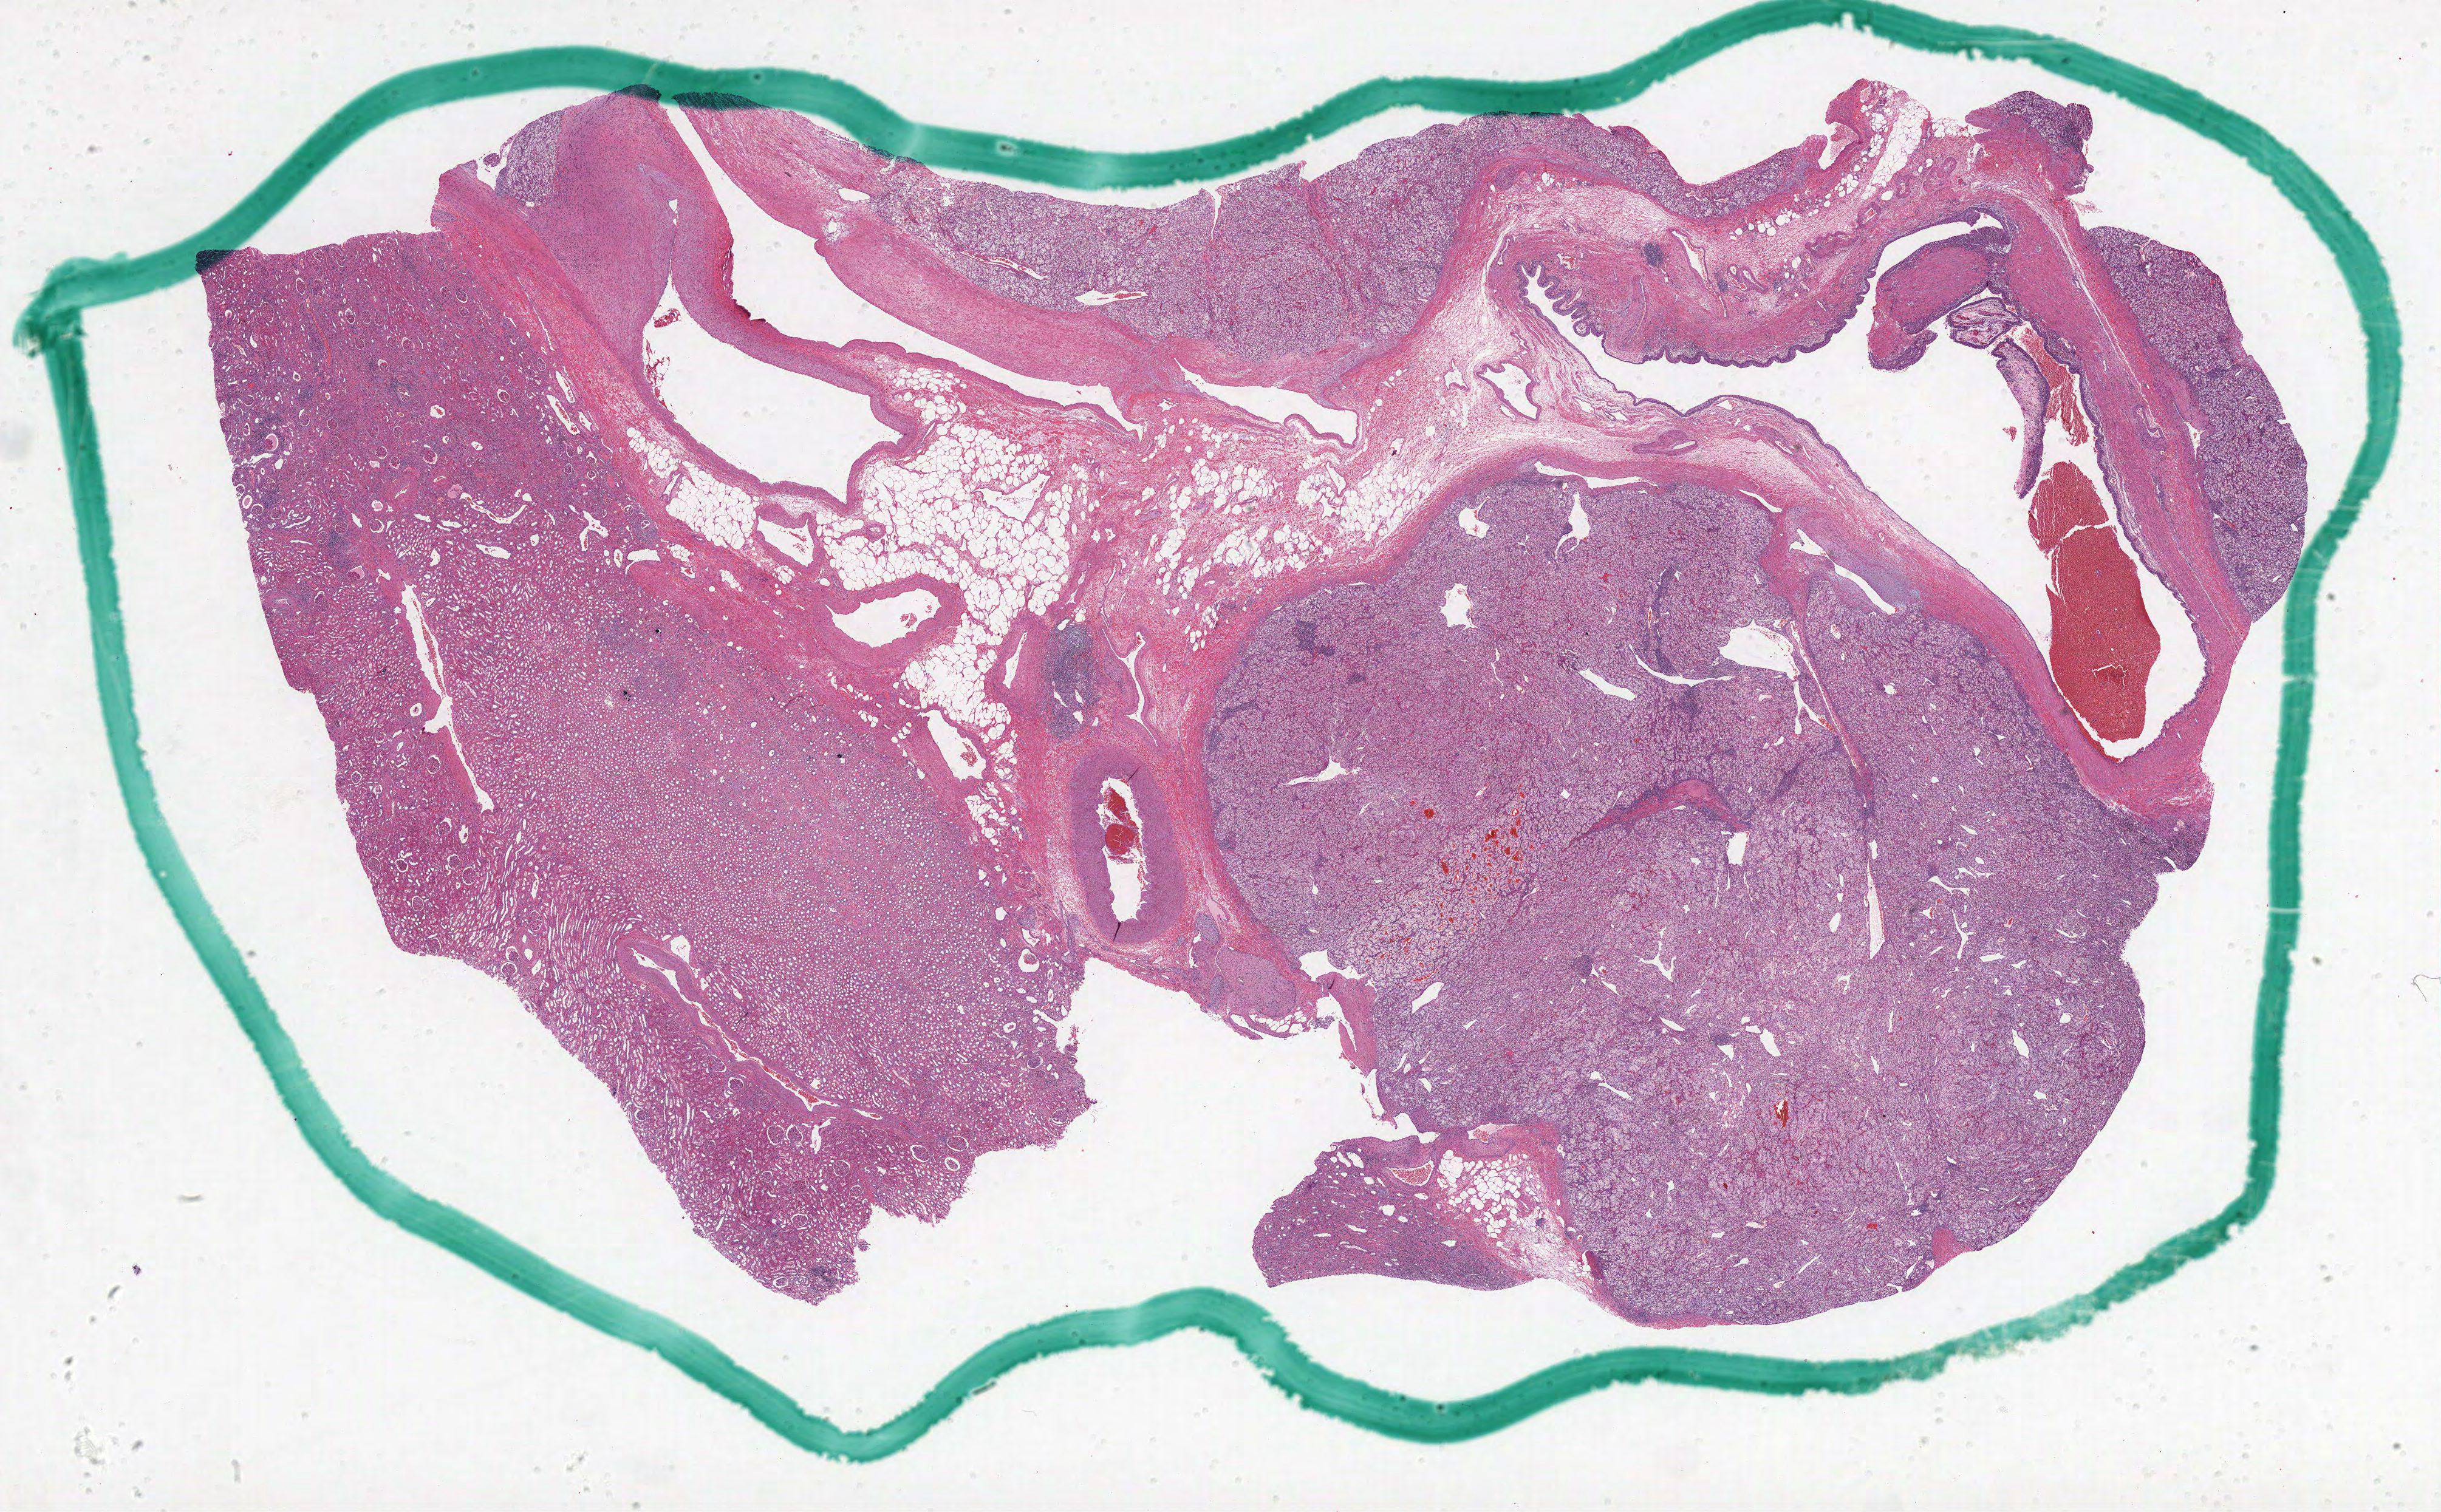
H&E whole-slide image, shown as a low-resolution overview of the whole scanned area (about 32.1 x 19.9 mm, from a 40x scan); FFPE section; primary tumour sample from the kidney. Male, age 47 years at initial diagnosis. Histologic grade: G3 (poorly differentiated).
Laterality: right. Diagnosis: Clear cell adenocarcinoma, NOS. AJCC pathologic stage: III.